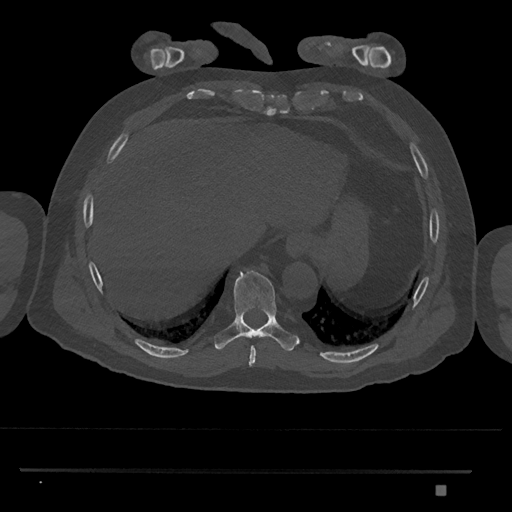
CT including the spine, one axial slice; position 1061 of 1134 along the scan axis; bone window (W 1800 / L 400 HU); 0.5 mm slice thickness; 512 × 512 image matrix, field of view 429 × 429 mm. Patient: male, 65 years. Case-level facts recorded for this patient, not image findings: primary cancer: prostate.
Outlined on this slice (semi-automatically segmented with operator editing):
- T8 vertebra: bounding box <248,346,256,366> (left, top, right, bottom; pixels)
- T9 vertebra: <214,270,300,352>